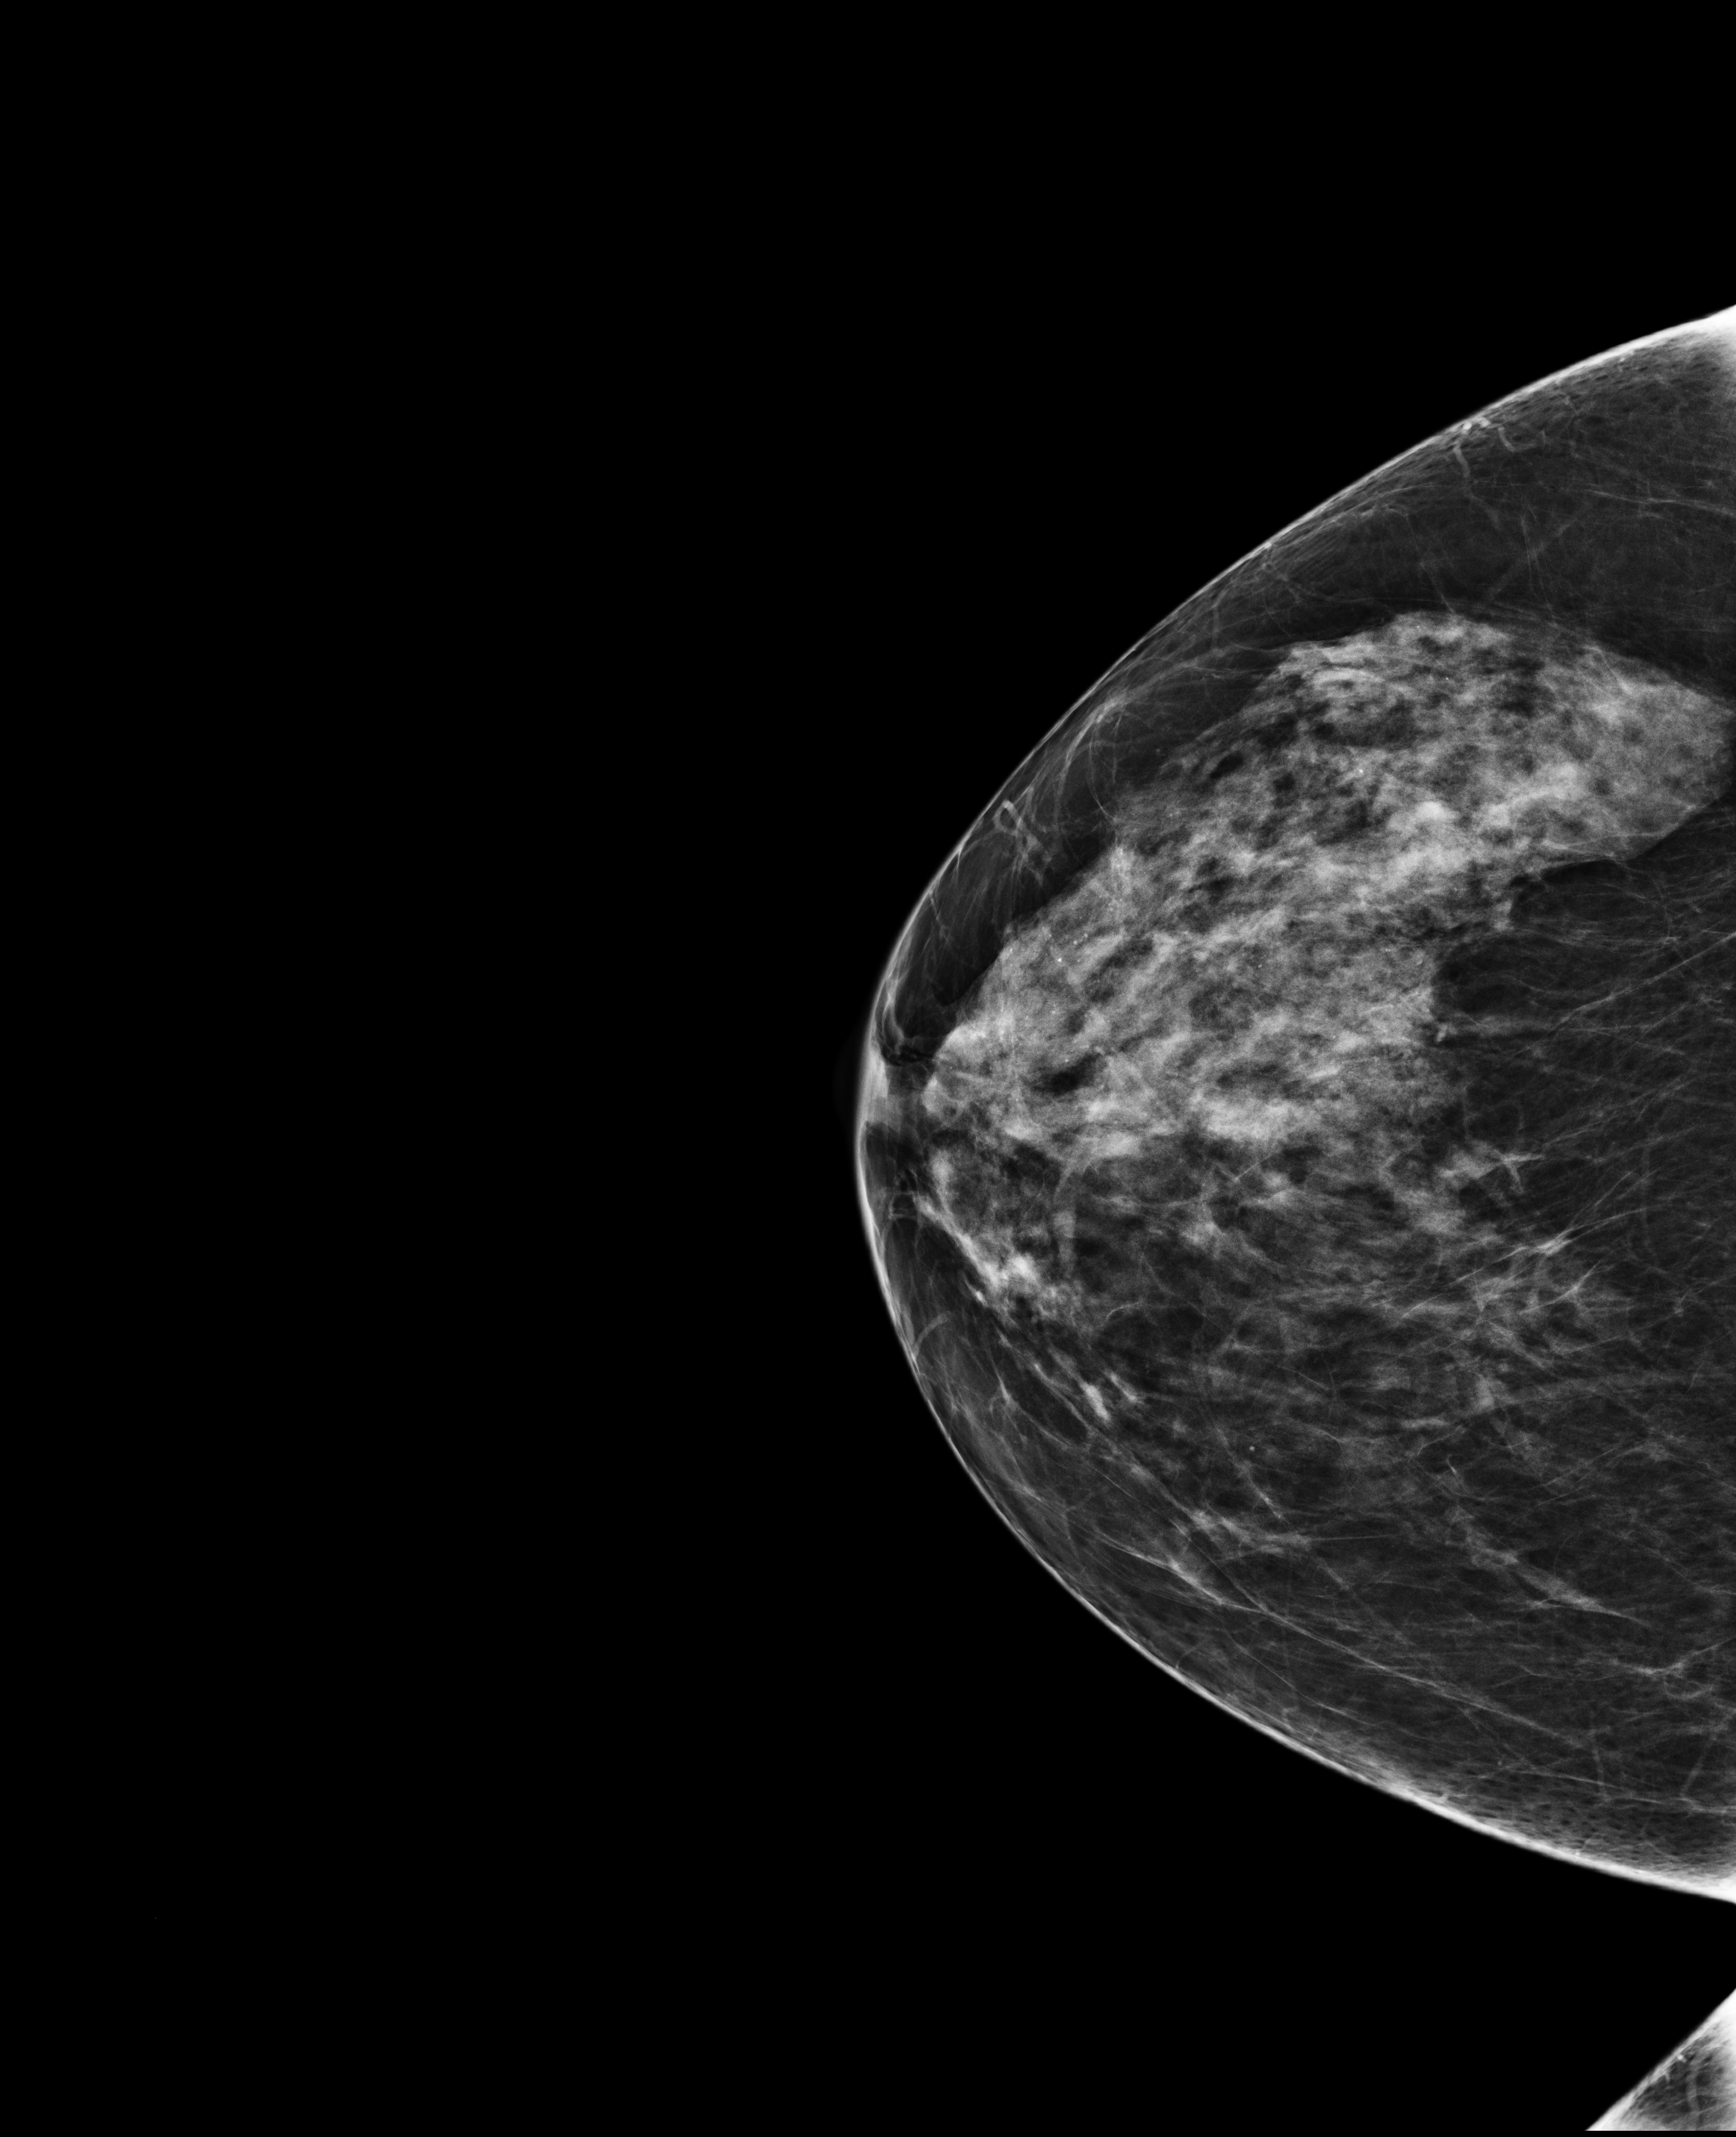
Full-field digital mammogram (FFDM); right breast; cranio-caudal projection; screening examination. Patient: female, 49 years.
- breast density at the screening exam (both breasts): heterogeneously dense (BI-RADS density category c)
- final BI-RADS assessment for this screening round (tomosynthesis exam, both breasts): category 2
- recall: no recall after this screen